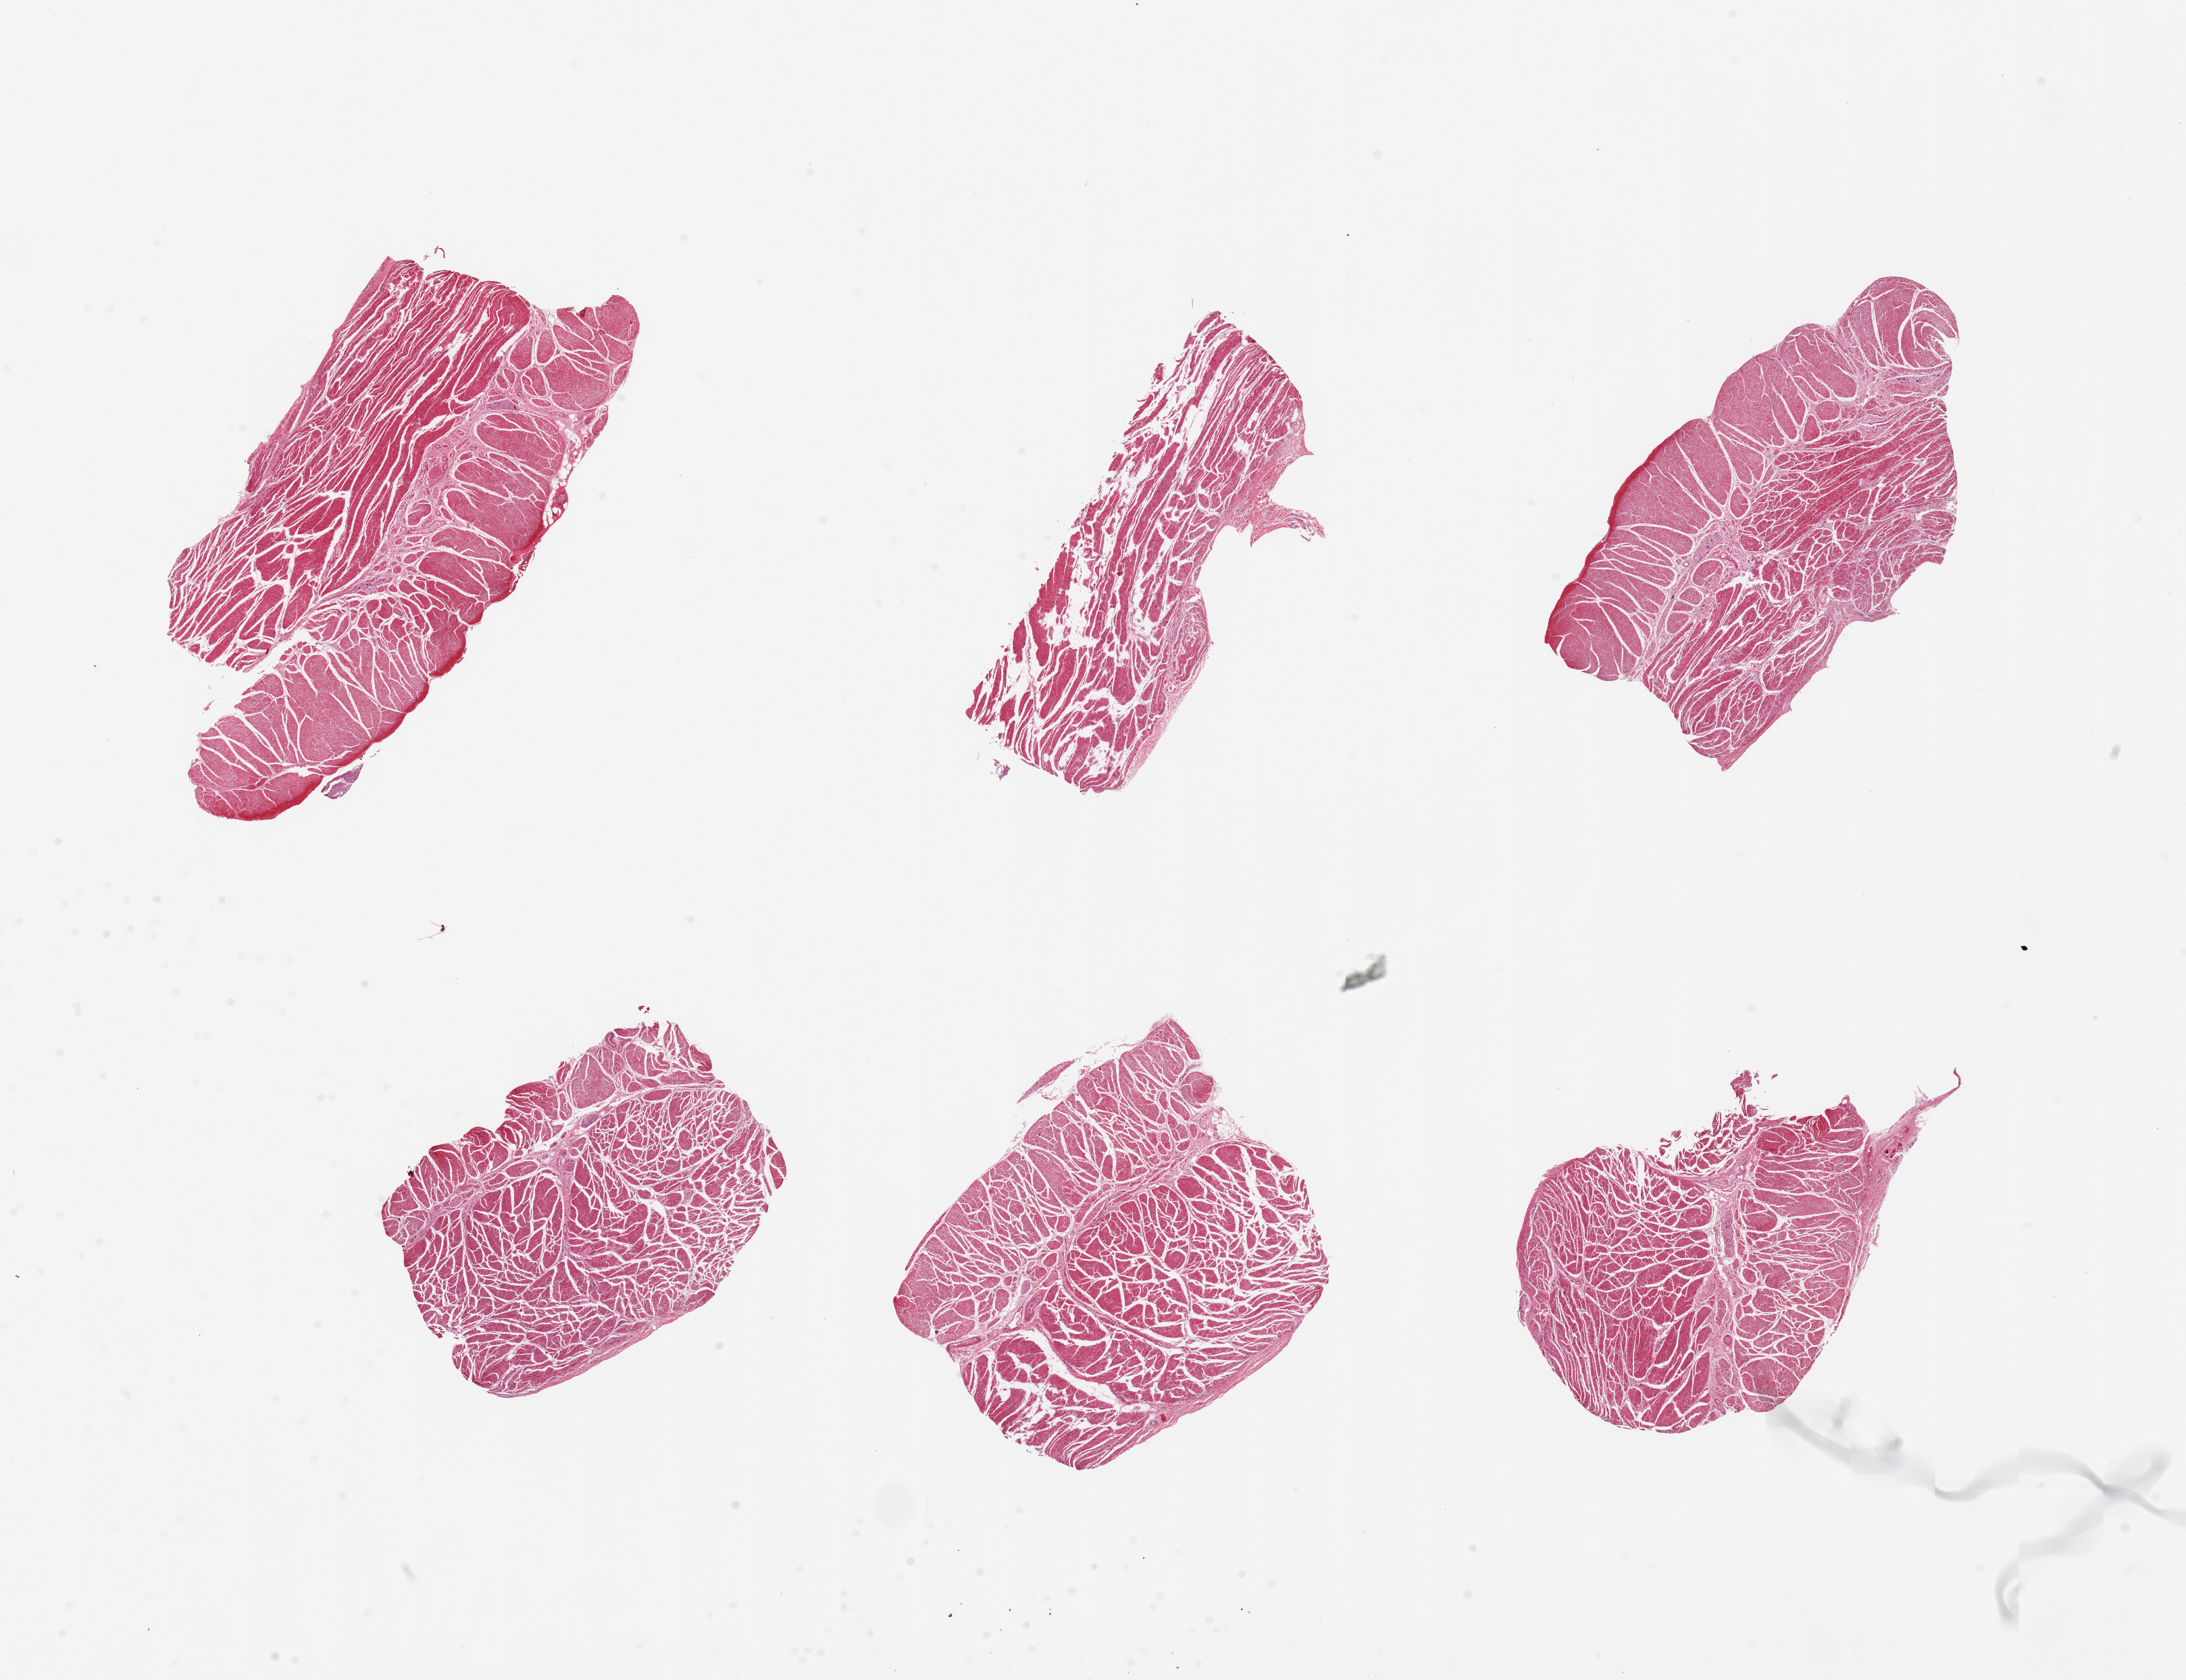
Haematoxylin and eosin whole-slide image, brightfield, whole scanned area (about 25.6 x 19.7 mm) shown as a low-resolution overview; PAXgene-fixed, paraffin-embedded tissue; target tissue: esophageal muscle; donor tissue sample. Donor: male.
- review note (as recorded): 6 pieces, all target muscularis